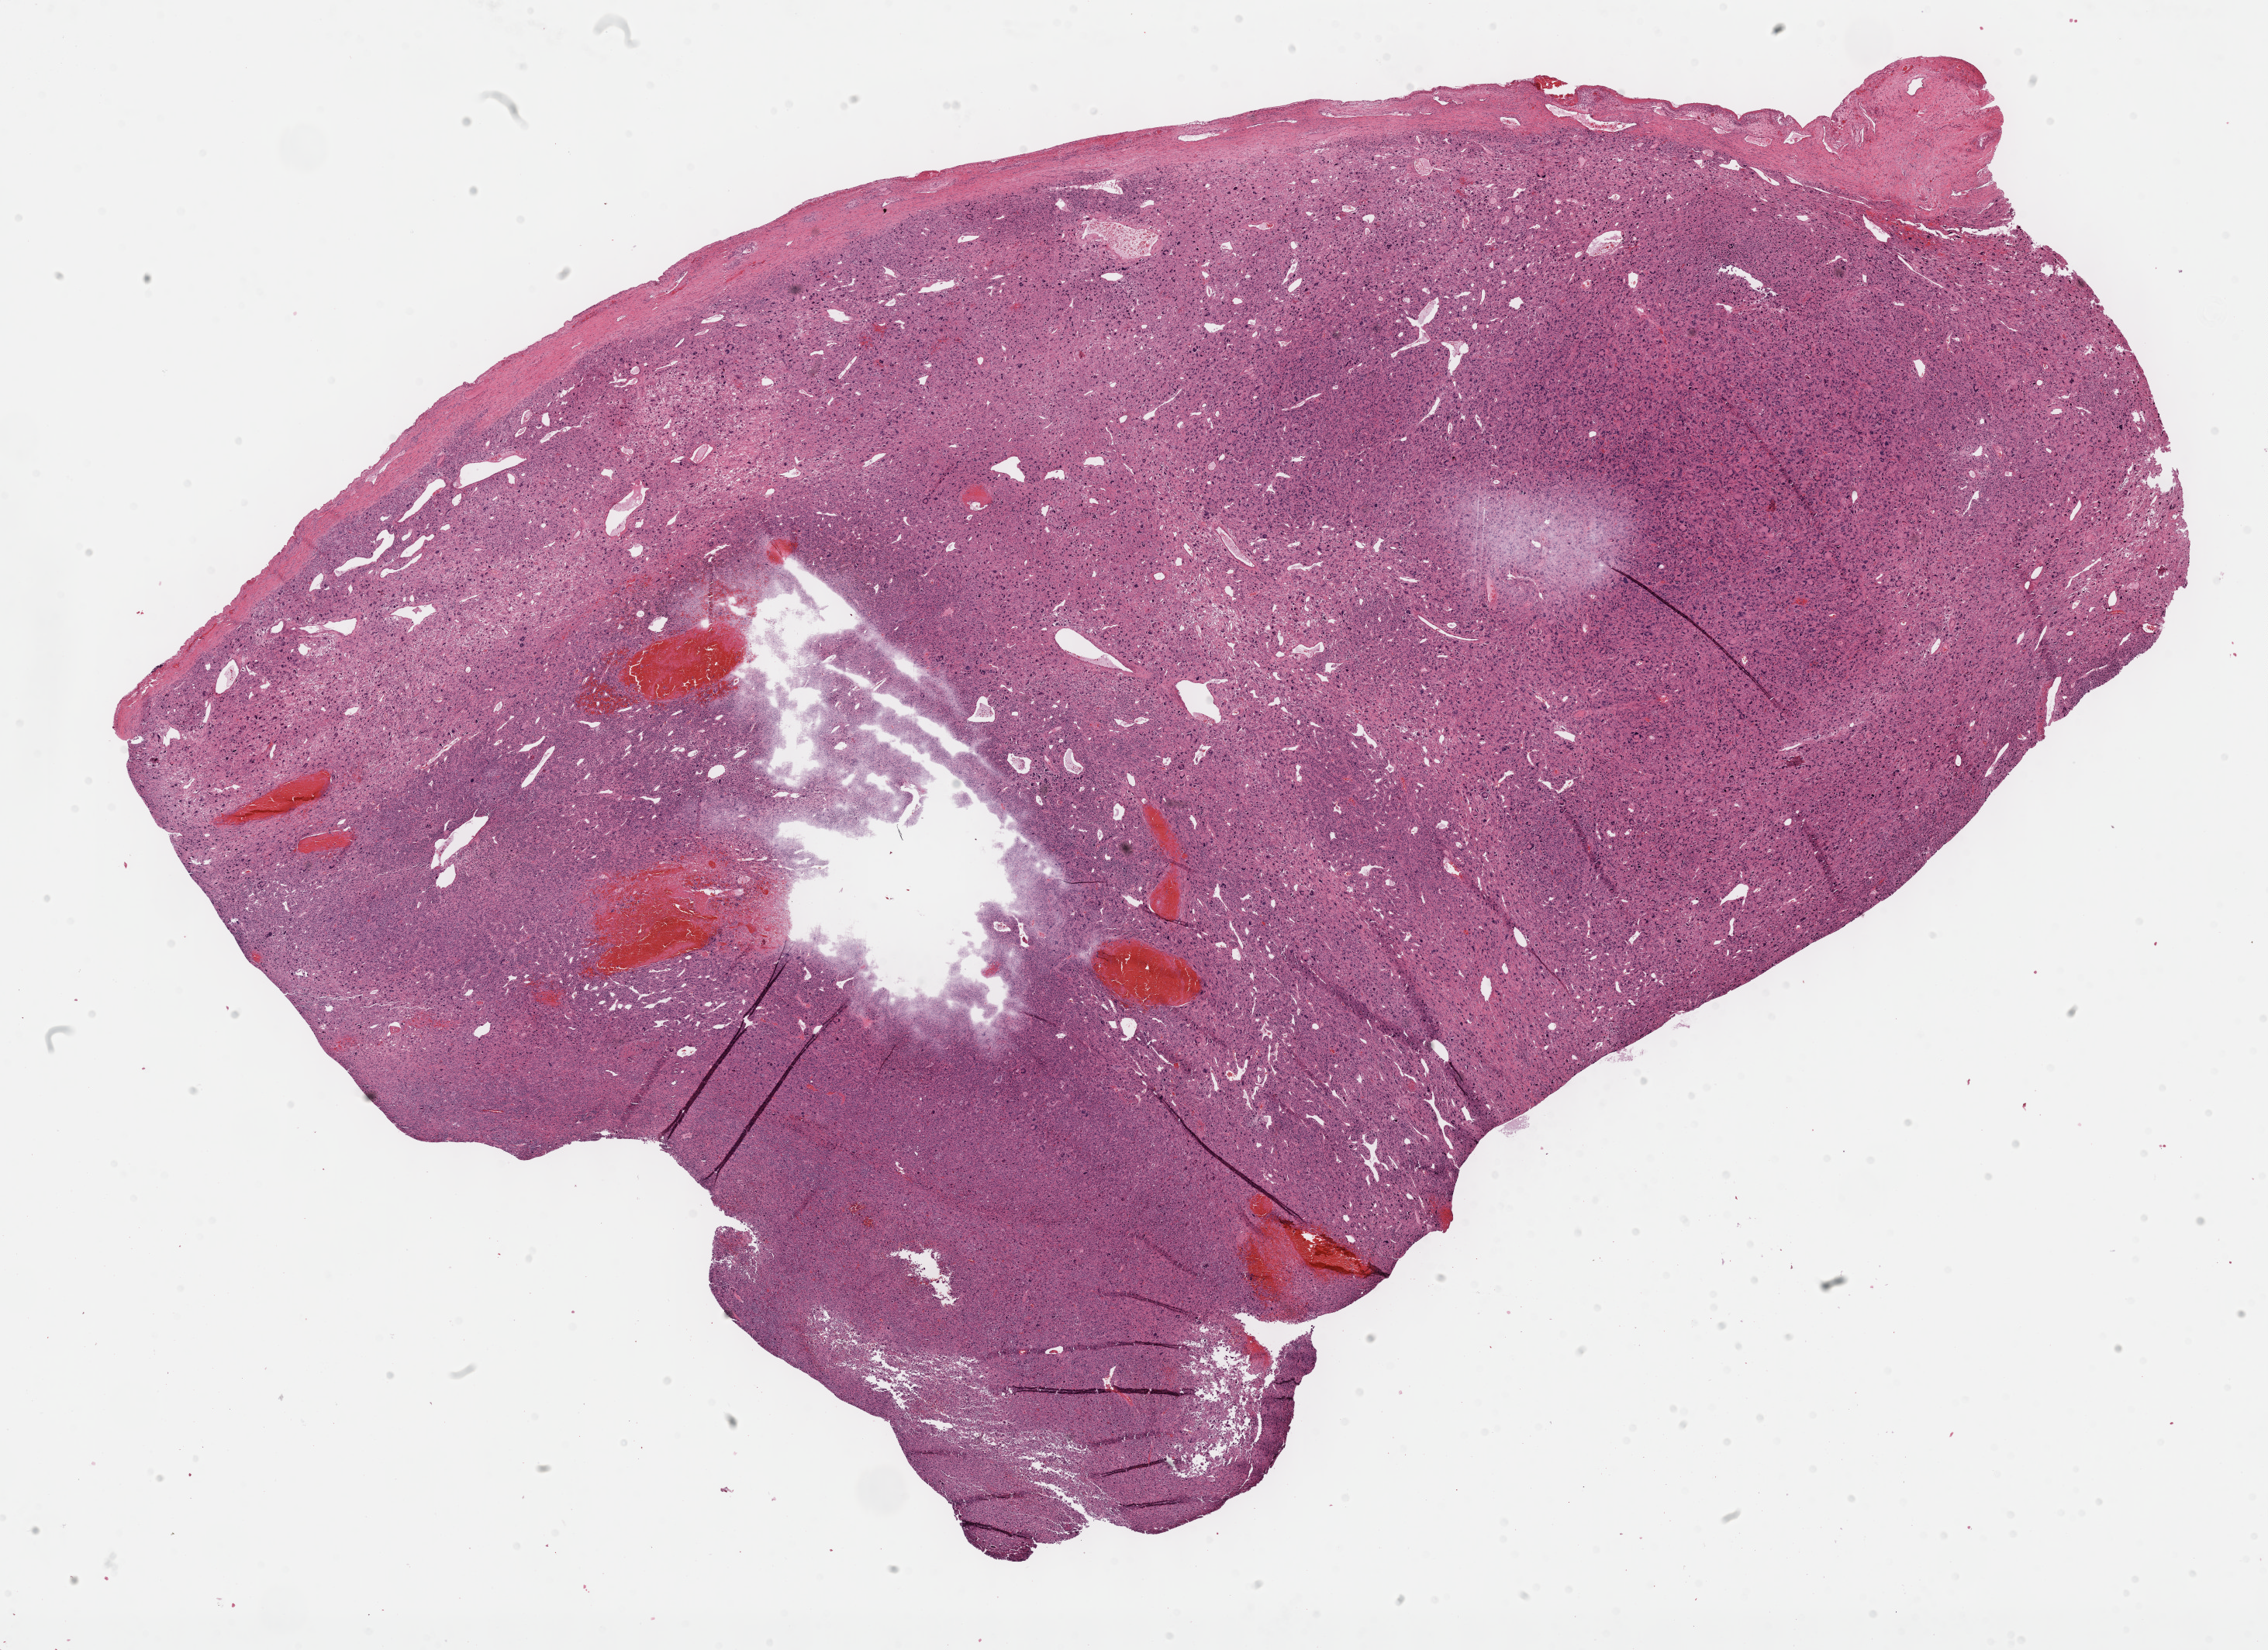
H&E-stained whole-slide image — whole scanned area (about 23.7 x 17.2 mm) shown as a low-resolution overview, FFPE section, primary tumour sample from the pancreas. Patient: female, age at initial diagnosis 58 years. Histologic grade: G4 (undifferentiated).
• lymph nodes positive (case pathology): 1 of 22 examined
• AJCC pathologic stage: IIB (7th edition)
• TNM: T3 N1 M0
• diagnosis: Carcinoma, undifferentiated, NOS (head of pancreas)